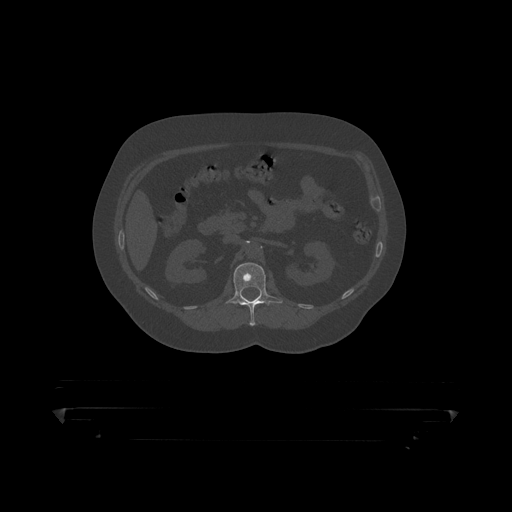
CT including the spine, one axial slice; slice 145 of 390 in the series (ordered by position); 120 kVp; bone window (W 1800 / L 400 HU); 1.25 mm slice thickness; 512 × 512 image matrix, field of view 650 × 650 mm. Patient: male, 60 years. Case-level facts recorded for this patient, not image findings: primary cancer: prostate.
Structures marked on this image (semi-automatic segmentation, software-assisted and operator-edited):
- L1 vertebra: bounding box [x1, y1, x2, y2] px = [224, 263, 283, 319]